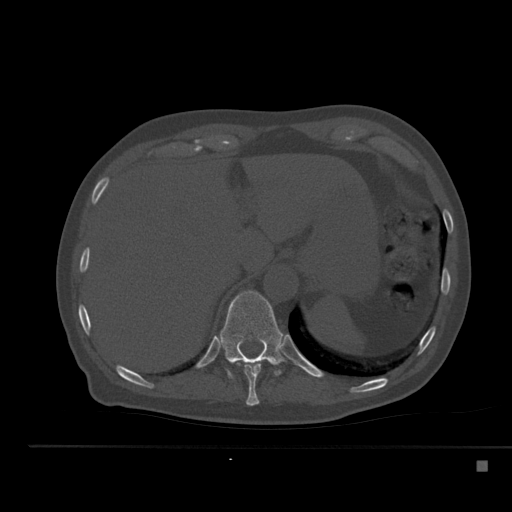
CT including the spine, one axial slice; slice 255 of 517 in the series (ordered by position); reconstruction kernel Br40s; 120 kVp; bone window (W 1800 / L 400 HU); 1.5 mm slice thickness; 512 × 512 image matrix. Male patient, age 70 years. Case-level facts recorded for this patient, not image findings: primary cancer: renal.
Structures marked on this image (semi-automatically segmented with operator editing):
- T10 vertebra: box from (x=238, y=360) to (x=263, y=406) px
- T11 vertebra: (x=218, y=290)–(x=285, y=378)